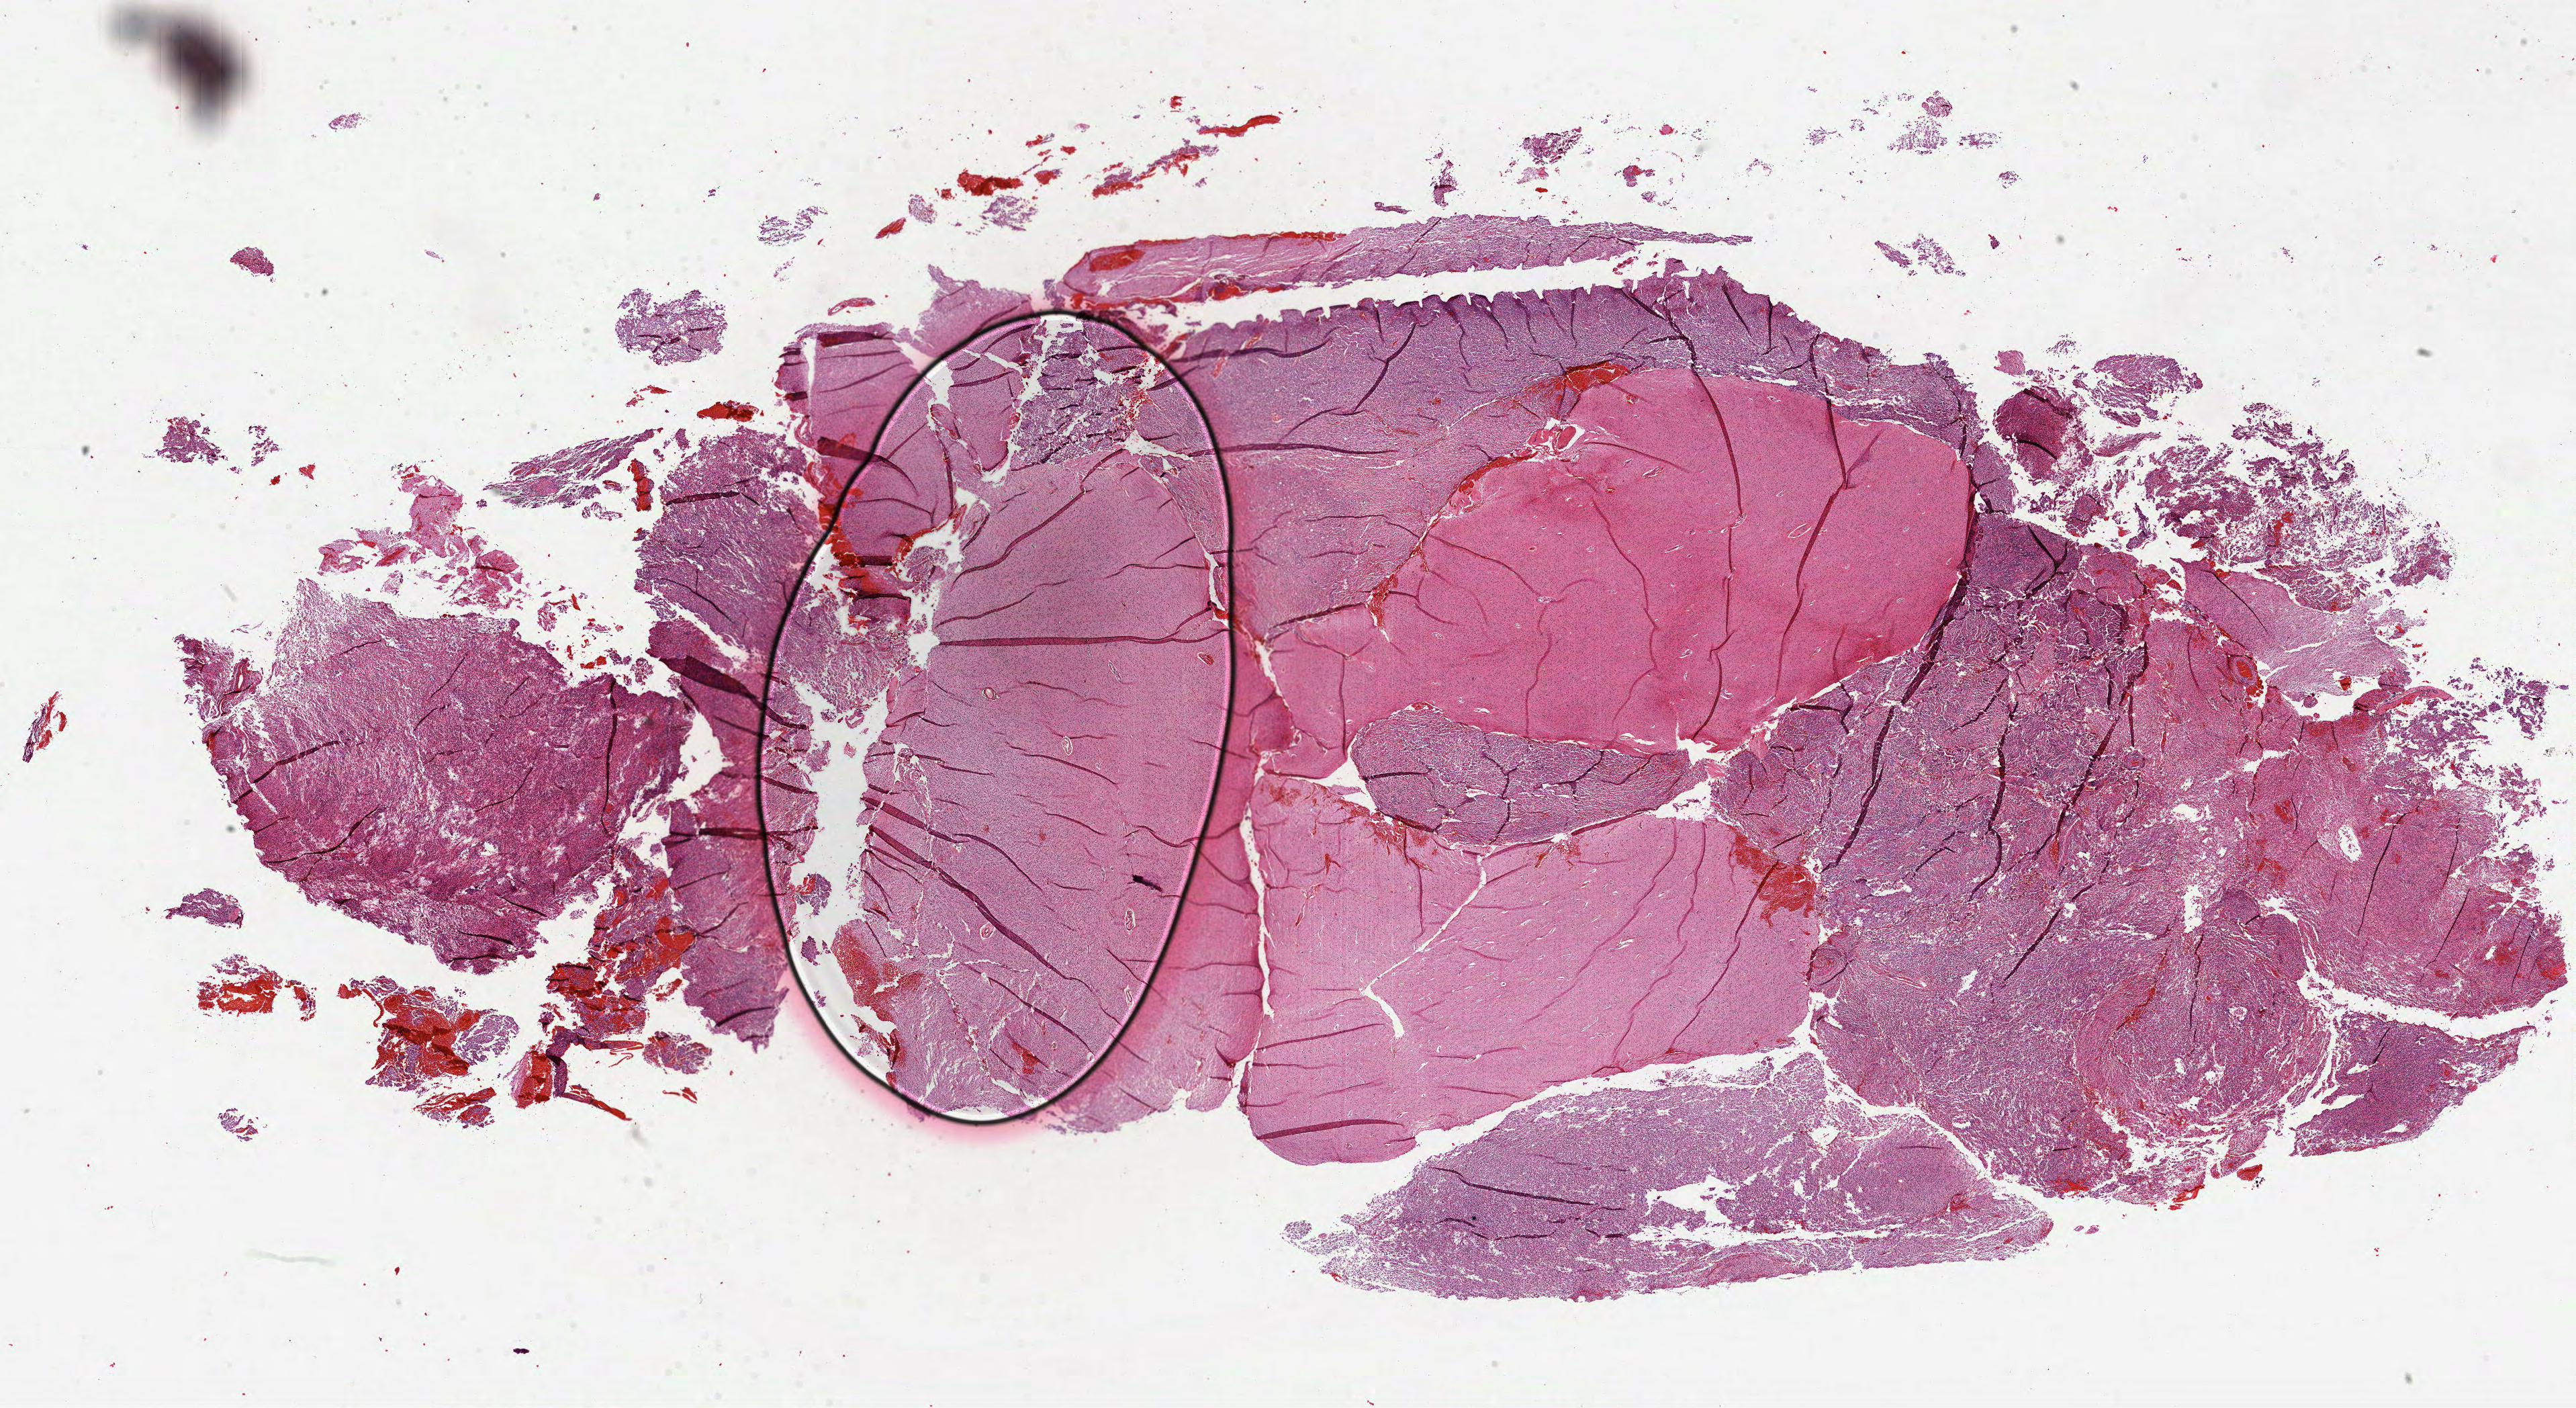
H&E whole-slide image — low-resolution overview of the scanned area, about 30.9 x 16.9 mm, formalin-fixed paraffin-embedded (FFPE) diagnostic section, sample: primary tumour, brain. Patient: male, age at initial diagnosis 43 years. Histologic grade: G3 (poorly differentiated).
Histologic diagnosis: Oligodendroglioma, anaplastic.